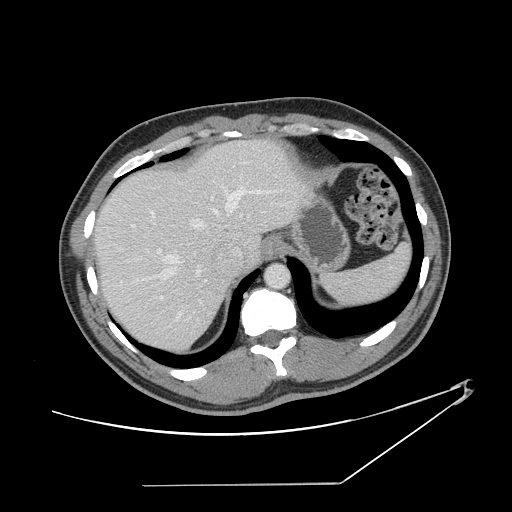
Contrast-enhanced abdominal CT, one axial slice. Position 116 of 152 along the scan axis. Reconstruction kernel STANDARD. Intravenous contrast given. Soft-tissue window (W 400 / L 40 HU). 512 × 512 image matrix, field of view 432 × 432 mm. Male patient, age 45 years. Case-level facts recorded for this patient, not image findings: diagnosis: colorectal cancer liver metastases, imaged before liver resection; multiple liver metastases: no; largest metastasis: 1 cm; chemotherapy before resection: yes.
Structures marked on this image (expert manual segmentation):
- hepatic veins: bounding box <118,185,277,279> (left, top, right, bottom; pixels)
- liver: <96,140,305,351>
- planned liver remnant (the part of the liver to remain after resection): <97,163,233,351>
- portal vein (with intrahepatic branches): <158,249,207,321>